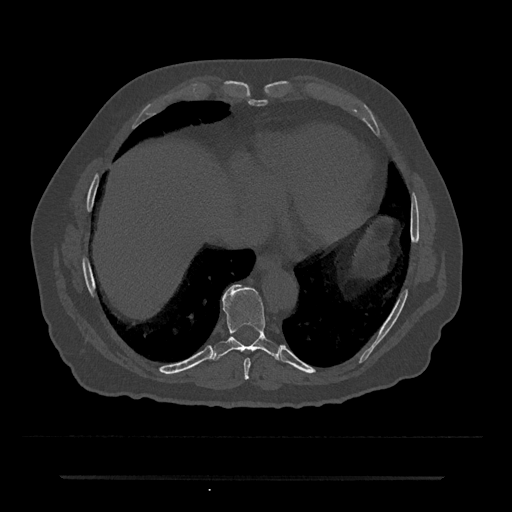
CT including the spine, one axial slice; position 286 of 797 along the scan axis; reconstruction kernel Br40s/3; bone window (W 1800 / L 400 HU); 0.5 mm slice thickness; 512 × 512 image matrix, field of view 437 × 437 mm. Male patient, age 69 years. Case-level facts recorded for this patient, not image findings: primary cancer: prostate.
Annotated regions visible in this slice (semi-automatically segmented with operator editing):
- T8 vertebra: bounding box (x1, y1, x2, y2) in pixels: (244, 358, 251, 379)
- T9 vertebra: (212, 284, 282, 361)